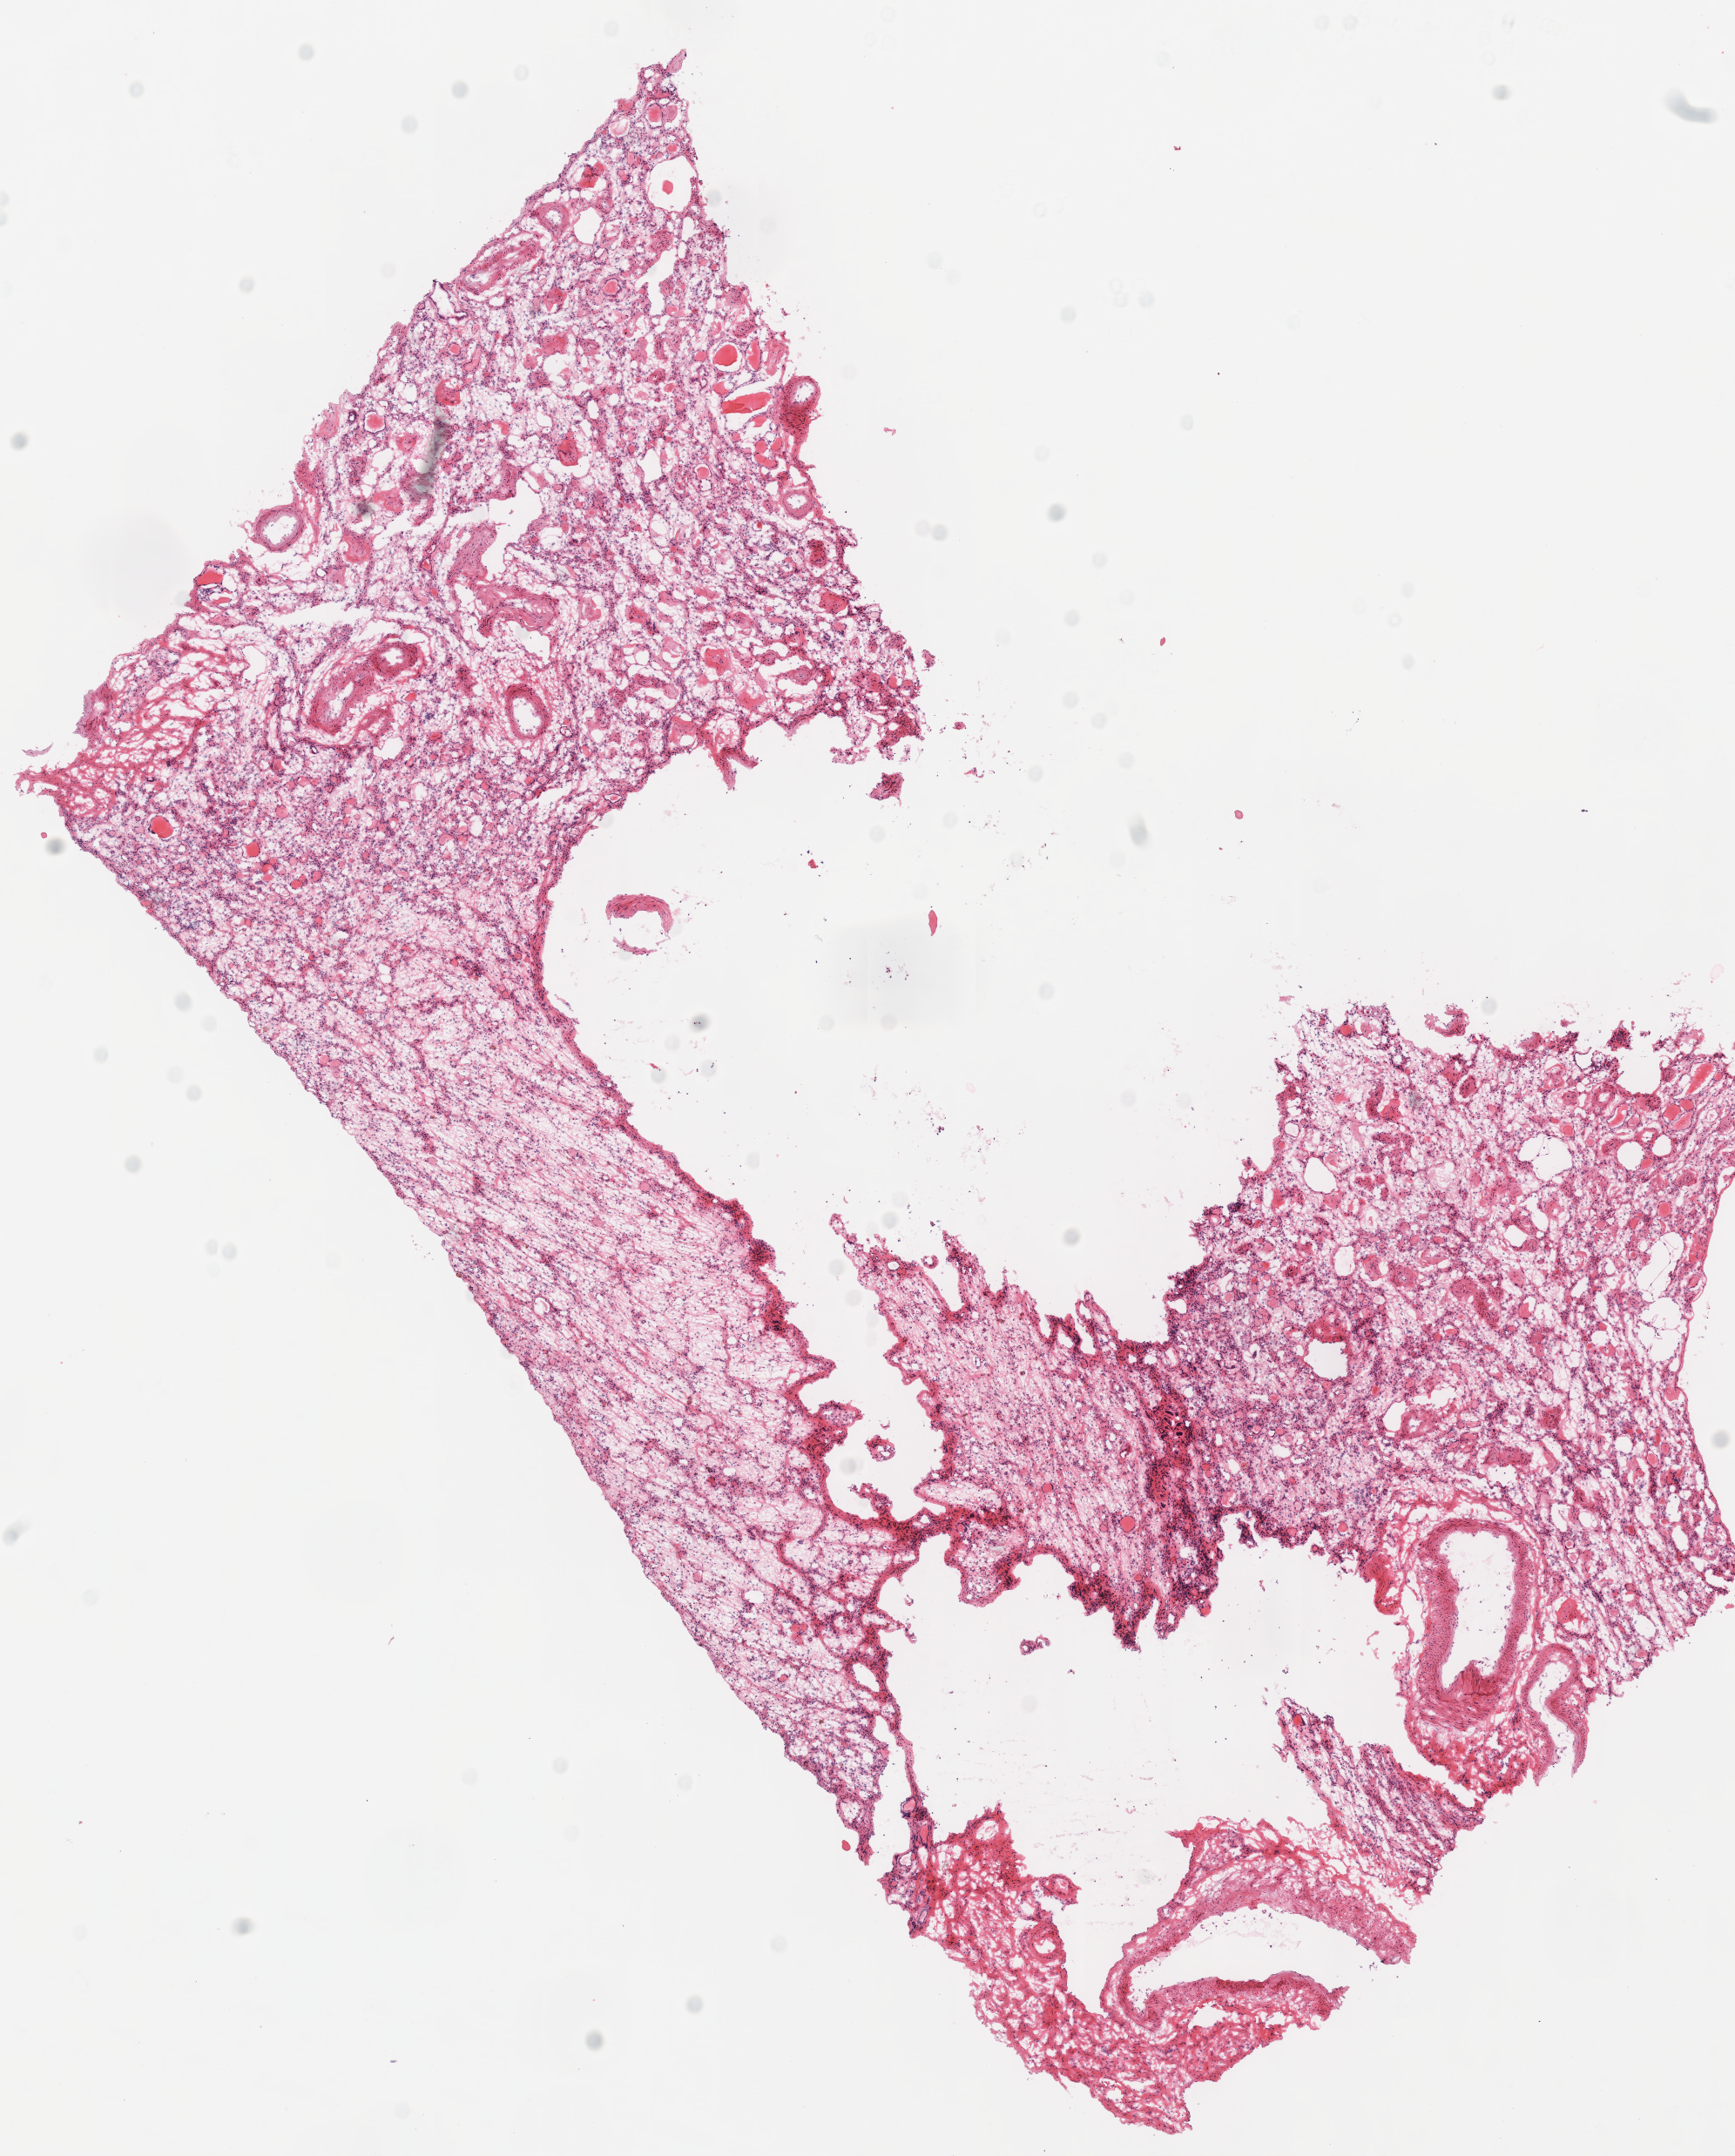
Digitized H&E-stained tissue section (whole slide), a low-resolution overview of the entire scanned area, about 7.8 x 9.7 mm, frozen section from the top of the tissue portion, kidney, solid tissue normal (non-tumour tissue) sample. Female patient; age at initial diagnosis 42 years.
This section: solid tissue normal sample (biorepository sample class). Patient diagnosis: Renal cell carcinoma, chromophobe type.